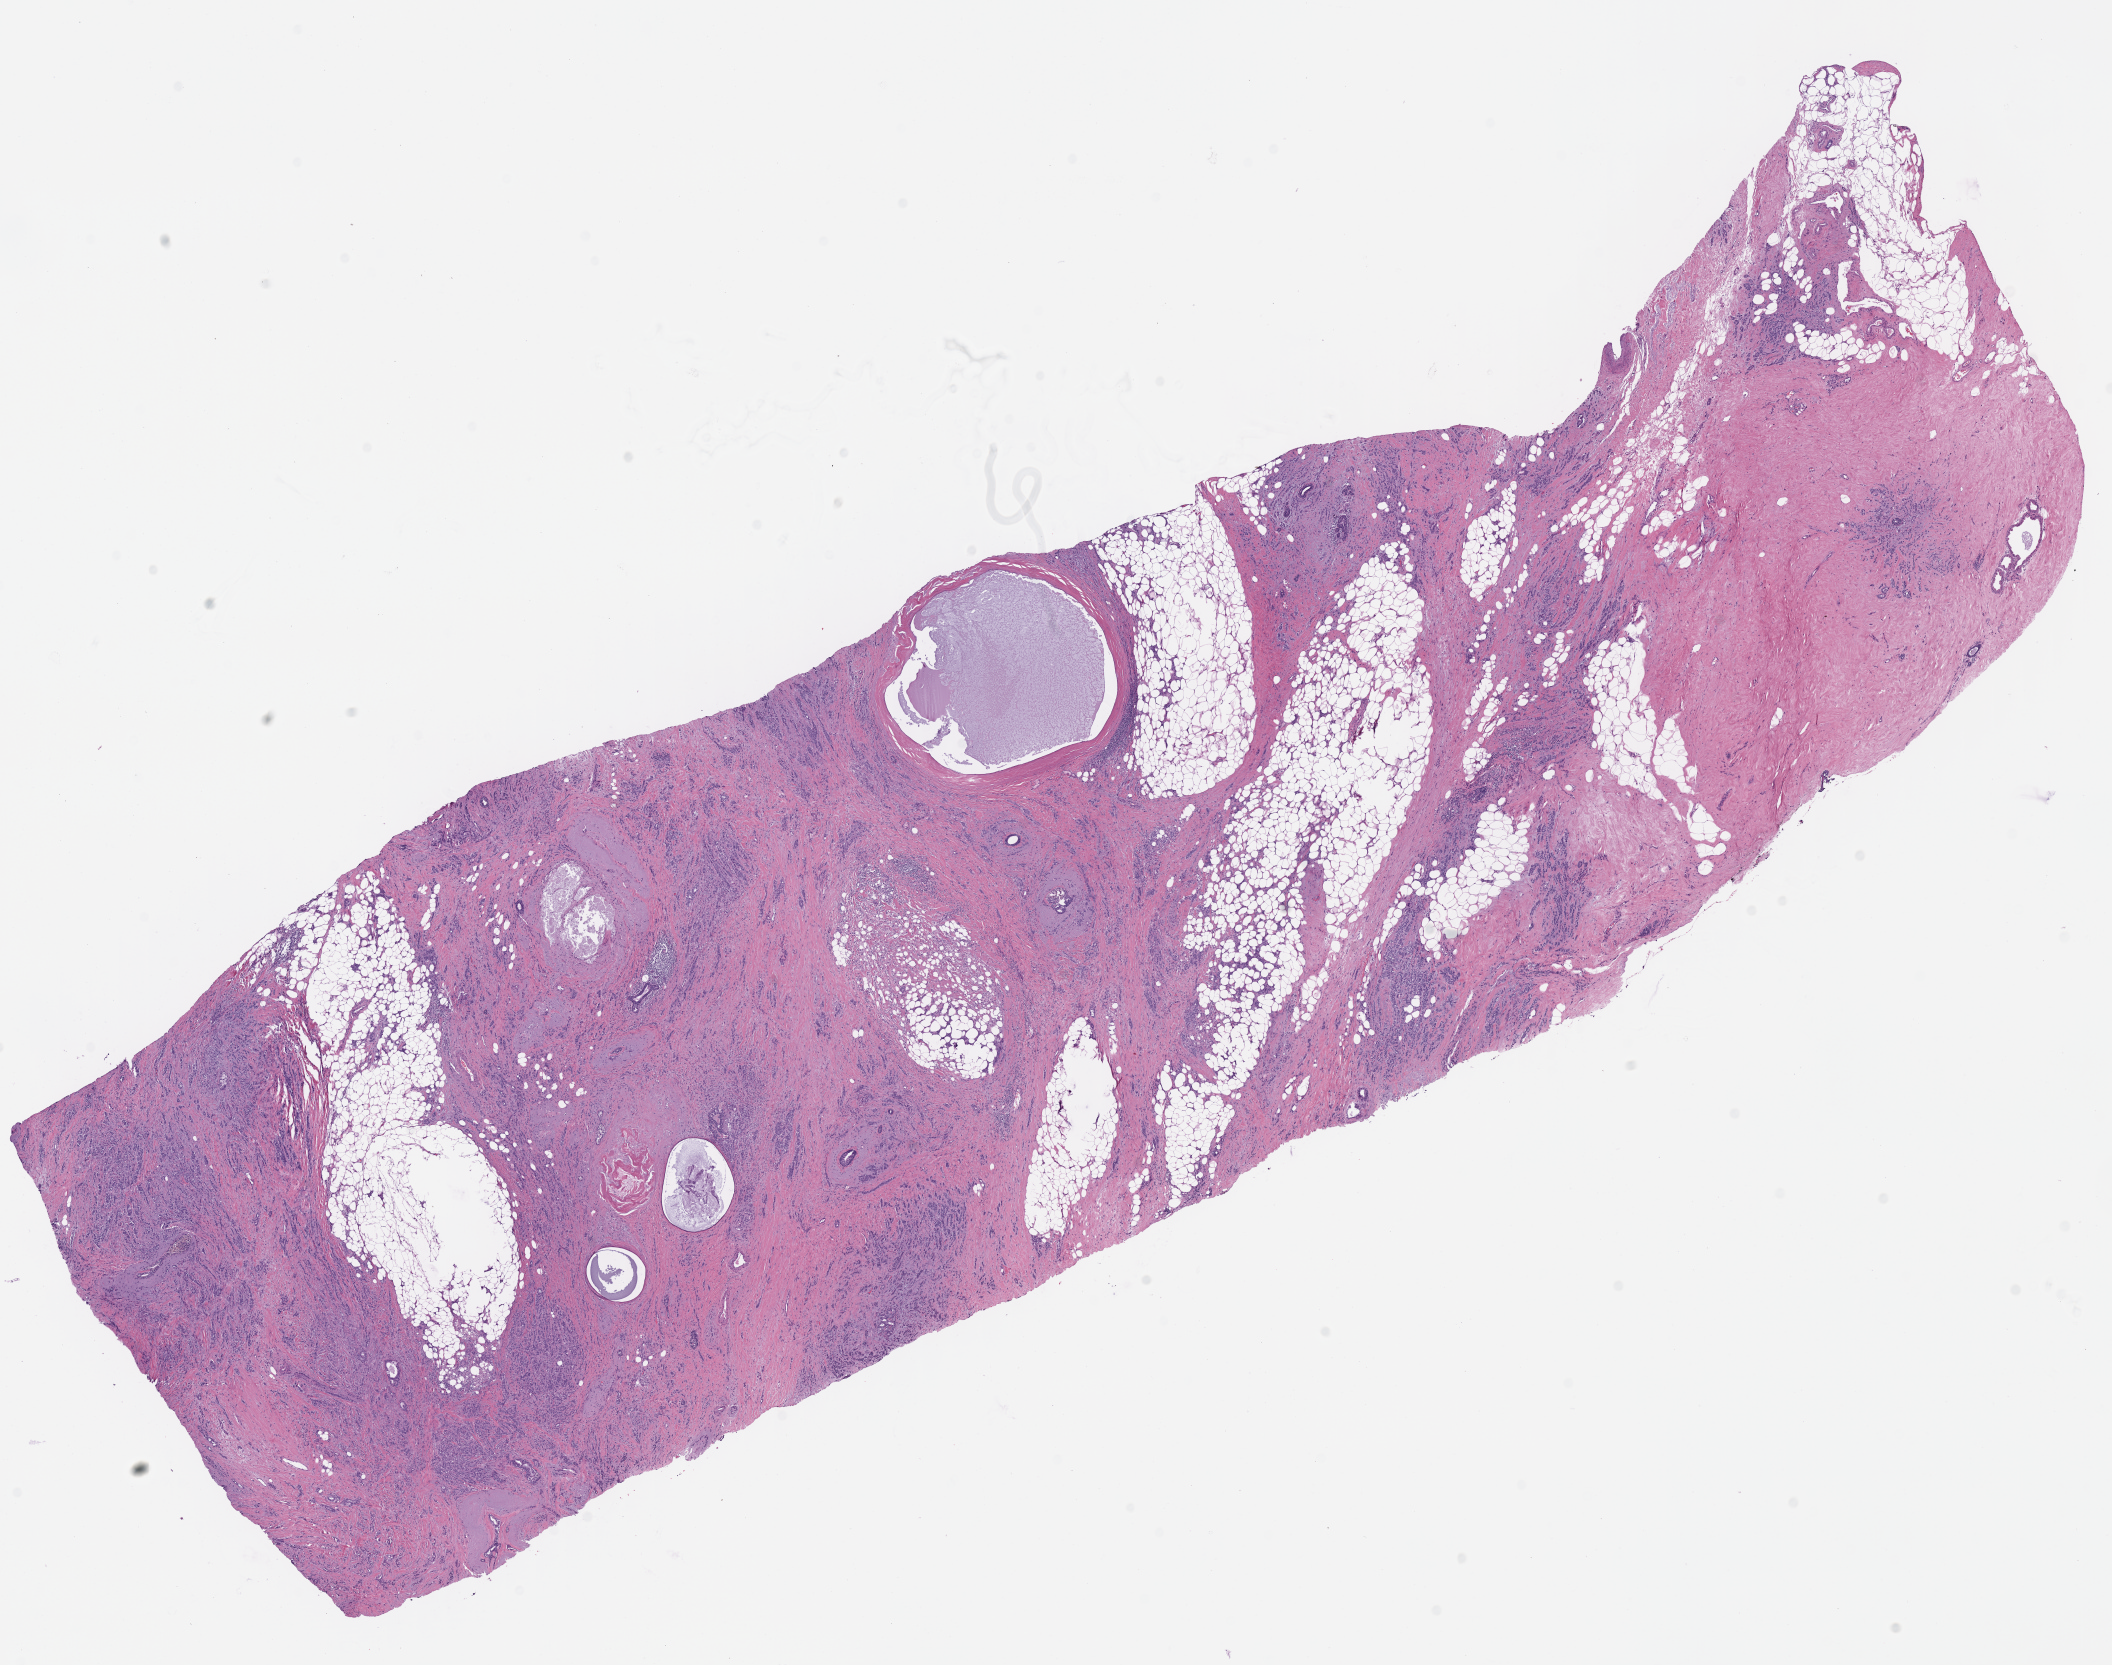
Digitized H&E-stained tissue section (whole slide) — a low-resolution overview of the entire scanned area, about 16.6 x 13.1 mm (acquisition: 40x scan), FFPE section, sample: primary tumour, breast. Female patient; age at initial diagnosis 84 years.
* diagnosis: Lobular carcinoma, NOS
* laterality: right
* lymph nodes positive (case pathology): 0 of 1 examined
* AJCC pathologic stage: IIB (7th edition)